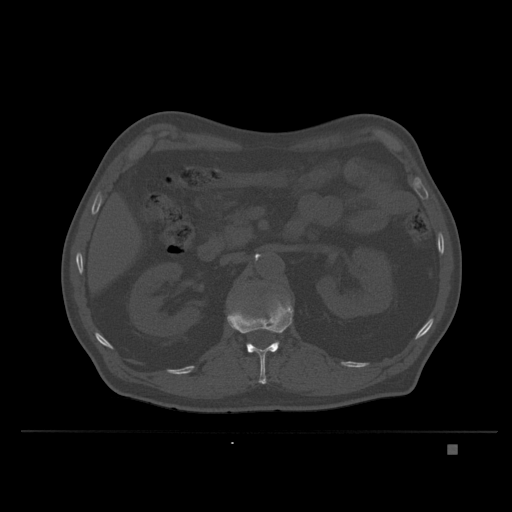
CT including the spine, one axial slice. Slice 134 of 435 in the series (ordered by position). Bone window (W 1800 / L 400 HU). 512 × 512 image matrix. Patient: male, 73 years. From the clinical record (not read from this slice): primary cancer: skin.
Annotated regions visible in this slice (semi-automatically segmented with operator editing):
- L1 vertebra: bounding box (x1, y1, x2, y2) in pixels: (227, 296, 294, 384)